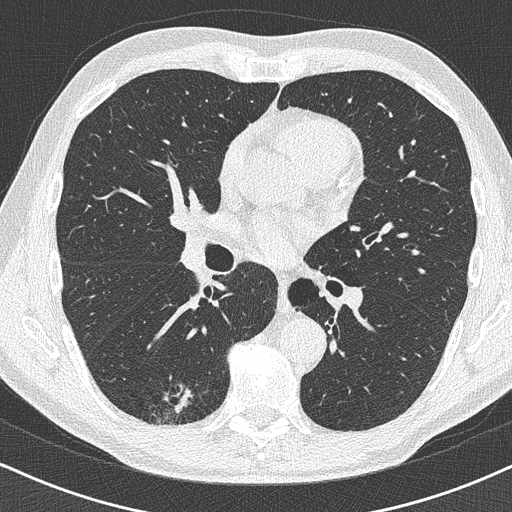
Chest CT (low-dose screening protocol), one axial image; baseline annual screen; lung window (W 1500 / L -600 HU); 1 mm slice thickness; lung (sharp) reconstruction kernel (B50f); slice 206 of 438 in the series. Male, age 63 years at enrolment. Former smoker at enrolment.
- Expert-annotated lung lesion, box from (x=139, y=374) to (x=210, y=430) px.
- The exam's reader record, not a measurement of the box and not confirmed to be the same lesion: non-calcified nodule or mass ≥4 mm, right lower lobe, 16 × 13 mm, poorly defined margins.
- Official screen result: positive, change unspecified: nodule(s) >= 4 mm or enlarging nodule(s), mass(es), or other non-specific abnormalities suspicious for lung cancer.
- Participant outcome: lung cancer diagnosed 74 days after this screen — adenocarcinoma, NOS, right lower lobe, moderately differentiated (G2), stage IA (AJCC 6th edition), 20 mm at pathology.